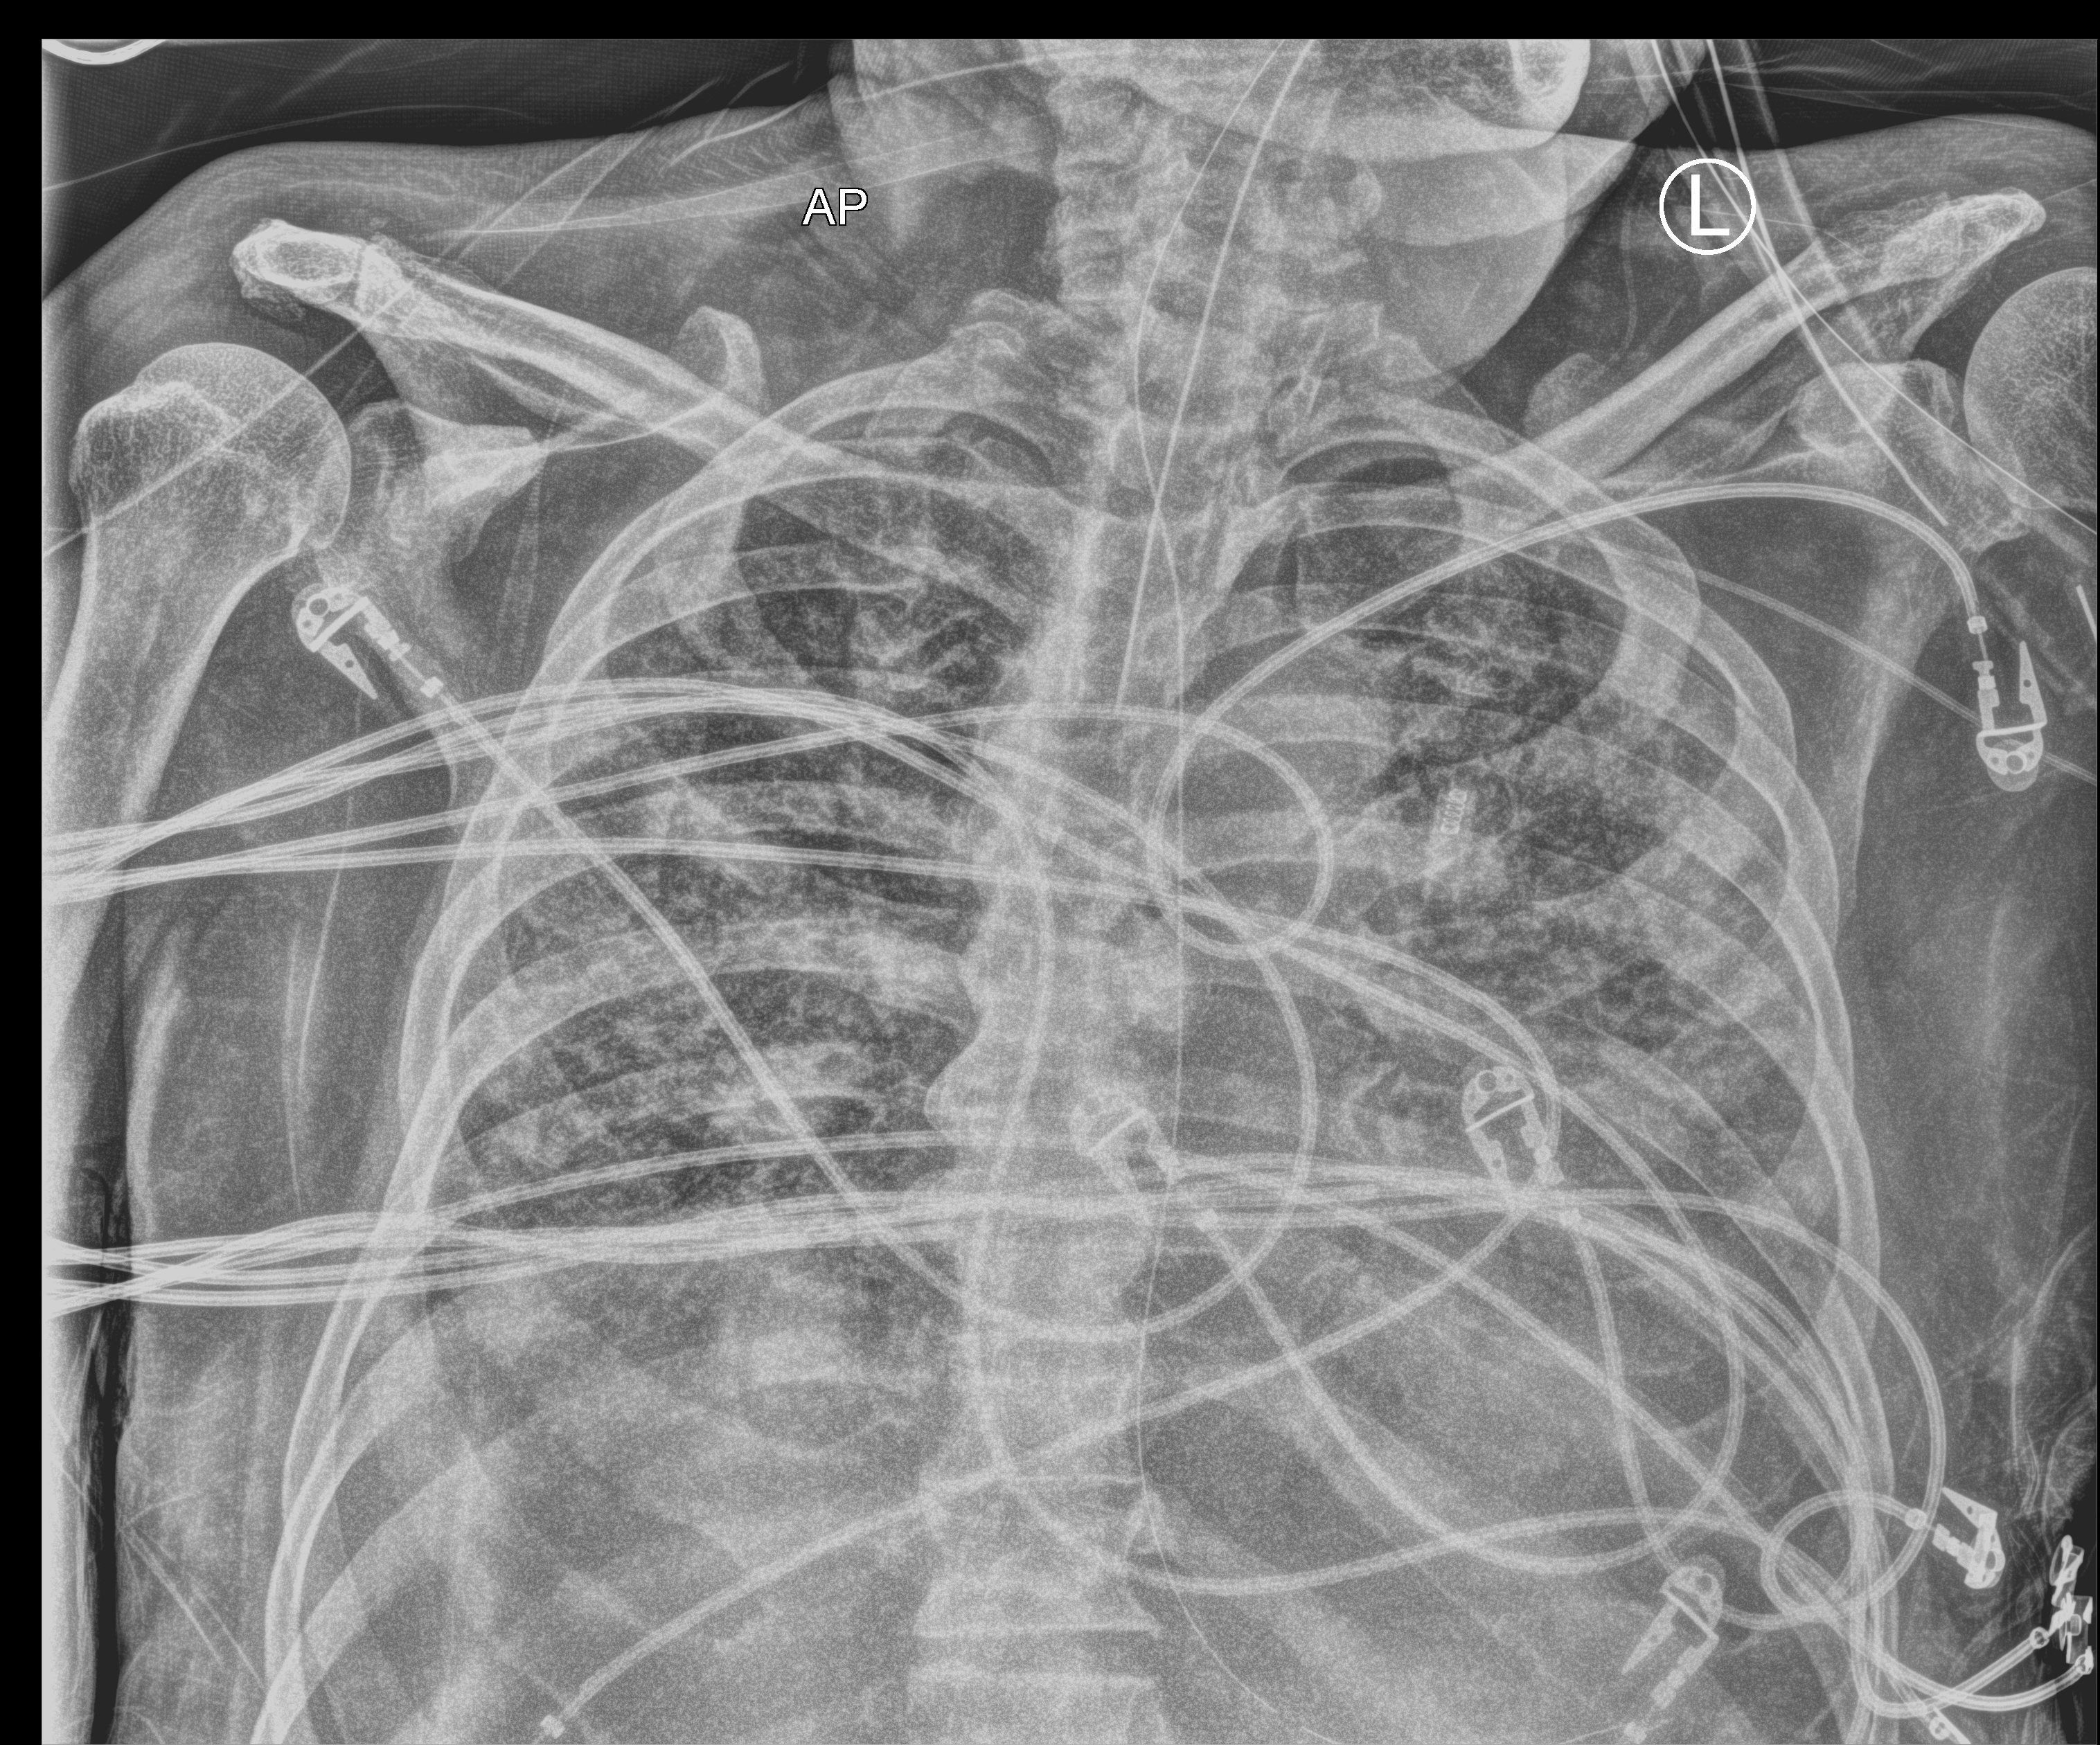
Bedside chest radiograph (computed radiography). Patient hospitalised with COVID-19; male, aged 75–90 years.
Admission-level facts for this patient (not findings on this image; timing relative to this image not recorded): chronic kidney disease (admission record): no; diabetes (admission record): no; admitted to intensive care during this hospital stay: yes.